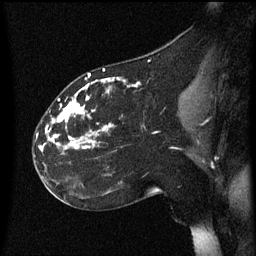
Breast MRI (dynamic contrast-enhanced), one sagittal slice; slice 31 of 60 in the series (ordered by position); dynamic contrast-enhanced series, image 2 of 3 at this slice position (ordered by acquisition); 1.5 T; TE 4.2 ms, TR 8.4 ms; 2.2 mm slice thickness; 256 × 256 image matrix, field of view 200 × 200 mm. Patient: female, 35 years. Case-level facts recorded for this patient, not image findings: setting: breast cancer imaged before/during neoadjuvant chemotherapy; receptor status: HER2-positive.
Outlined on this slice (semi-automatic segmentation, software-assisted and operator-edited):
- analysis volume of interest (the breast-tissue region the enhancement analysis was run in; not a lesion): bounding box [x1, y1, x2, y2] px = [33, 72, 168, 173]
- tumour enhancement mask (voxels above the 70 % enhancement threshold inside the analysis volume of interest): [37, 74, 141, 151]